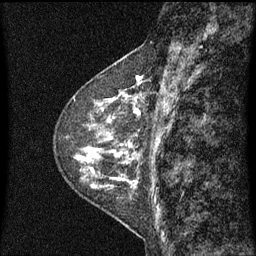
Breast MRI (dynamic contrast-enhanced), one sagittal slice. Slice 24 of 60 in the series (ordered by position). Dynamic contrast-enhanced series, image 2 of 3 at this slice position (ordered by acquisition). 1.5 T. TE 4.2 ms, TR 8 ms. 2 mm slice thickness. 256 × 256 image matrix, field of view 200 × 200 mm. Female patient, age 48 years.
Outlined on this slice (semi-automatically segmented with operator editing):
- analysis volume of interest (the breast-tissue region the enhancement analysis was run in; not a lesion): bounding box <103,74,145,139> (left, top, right, bottom; pixels)
- tumour enhancement mask (voxels above the 70 % enhancement threshold inside the analysis volume of interest): <115,76,143,137>